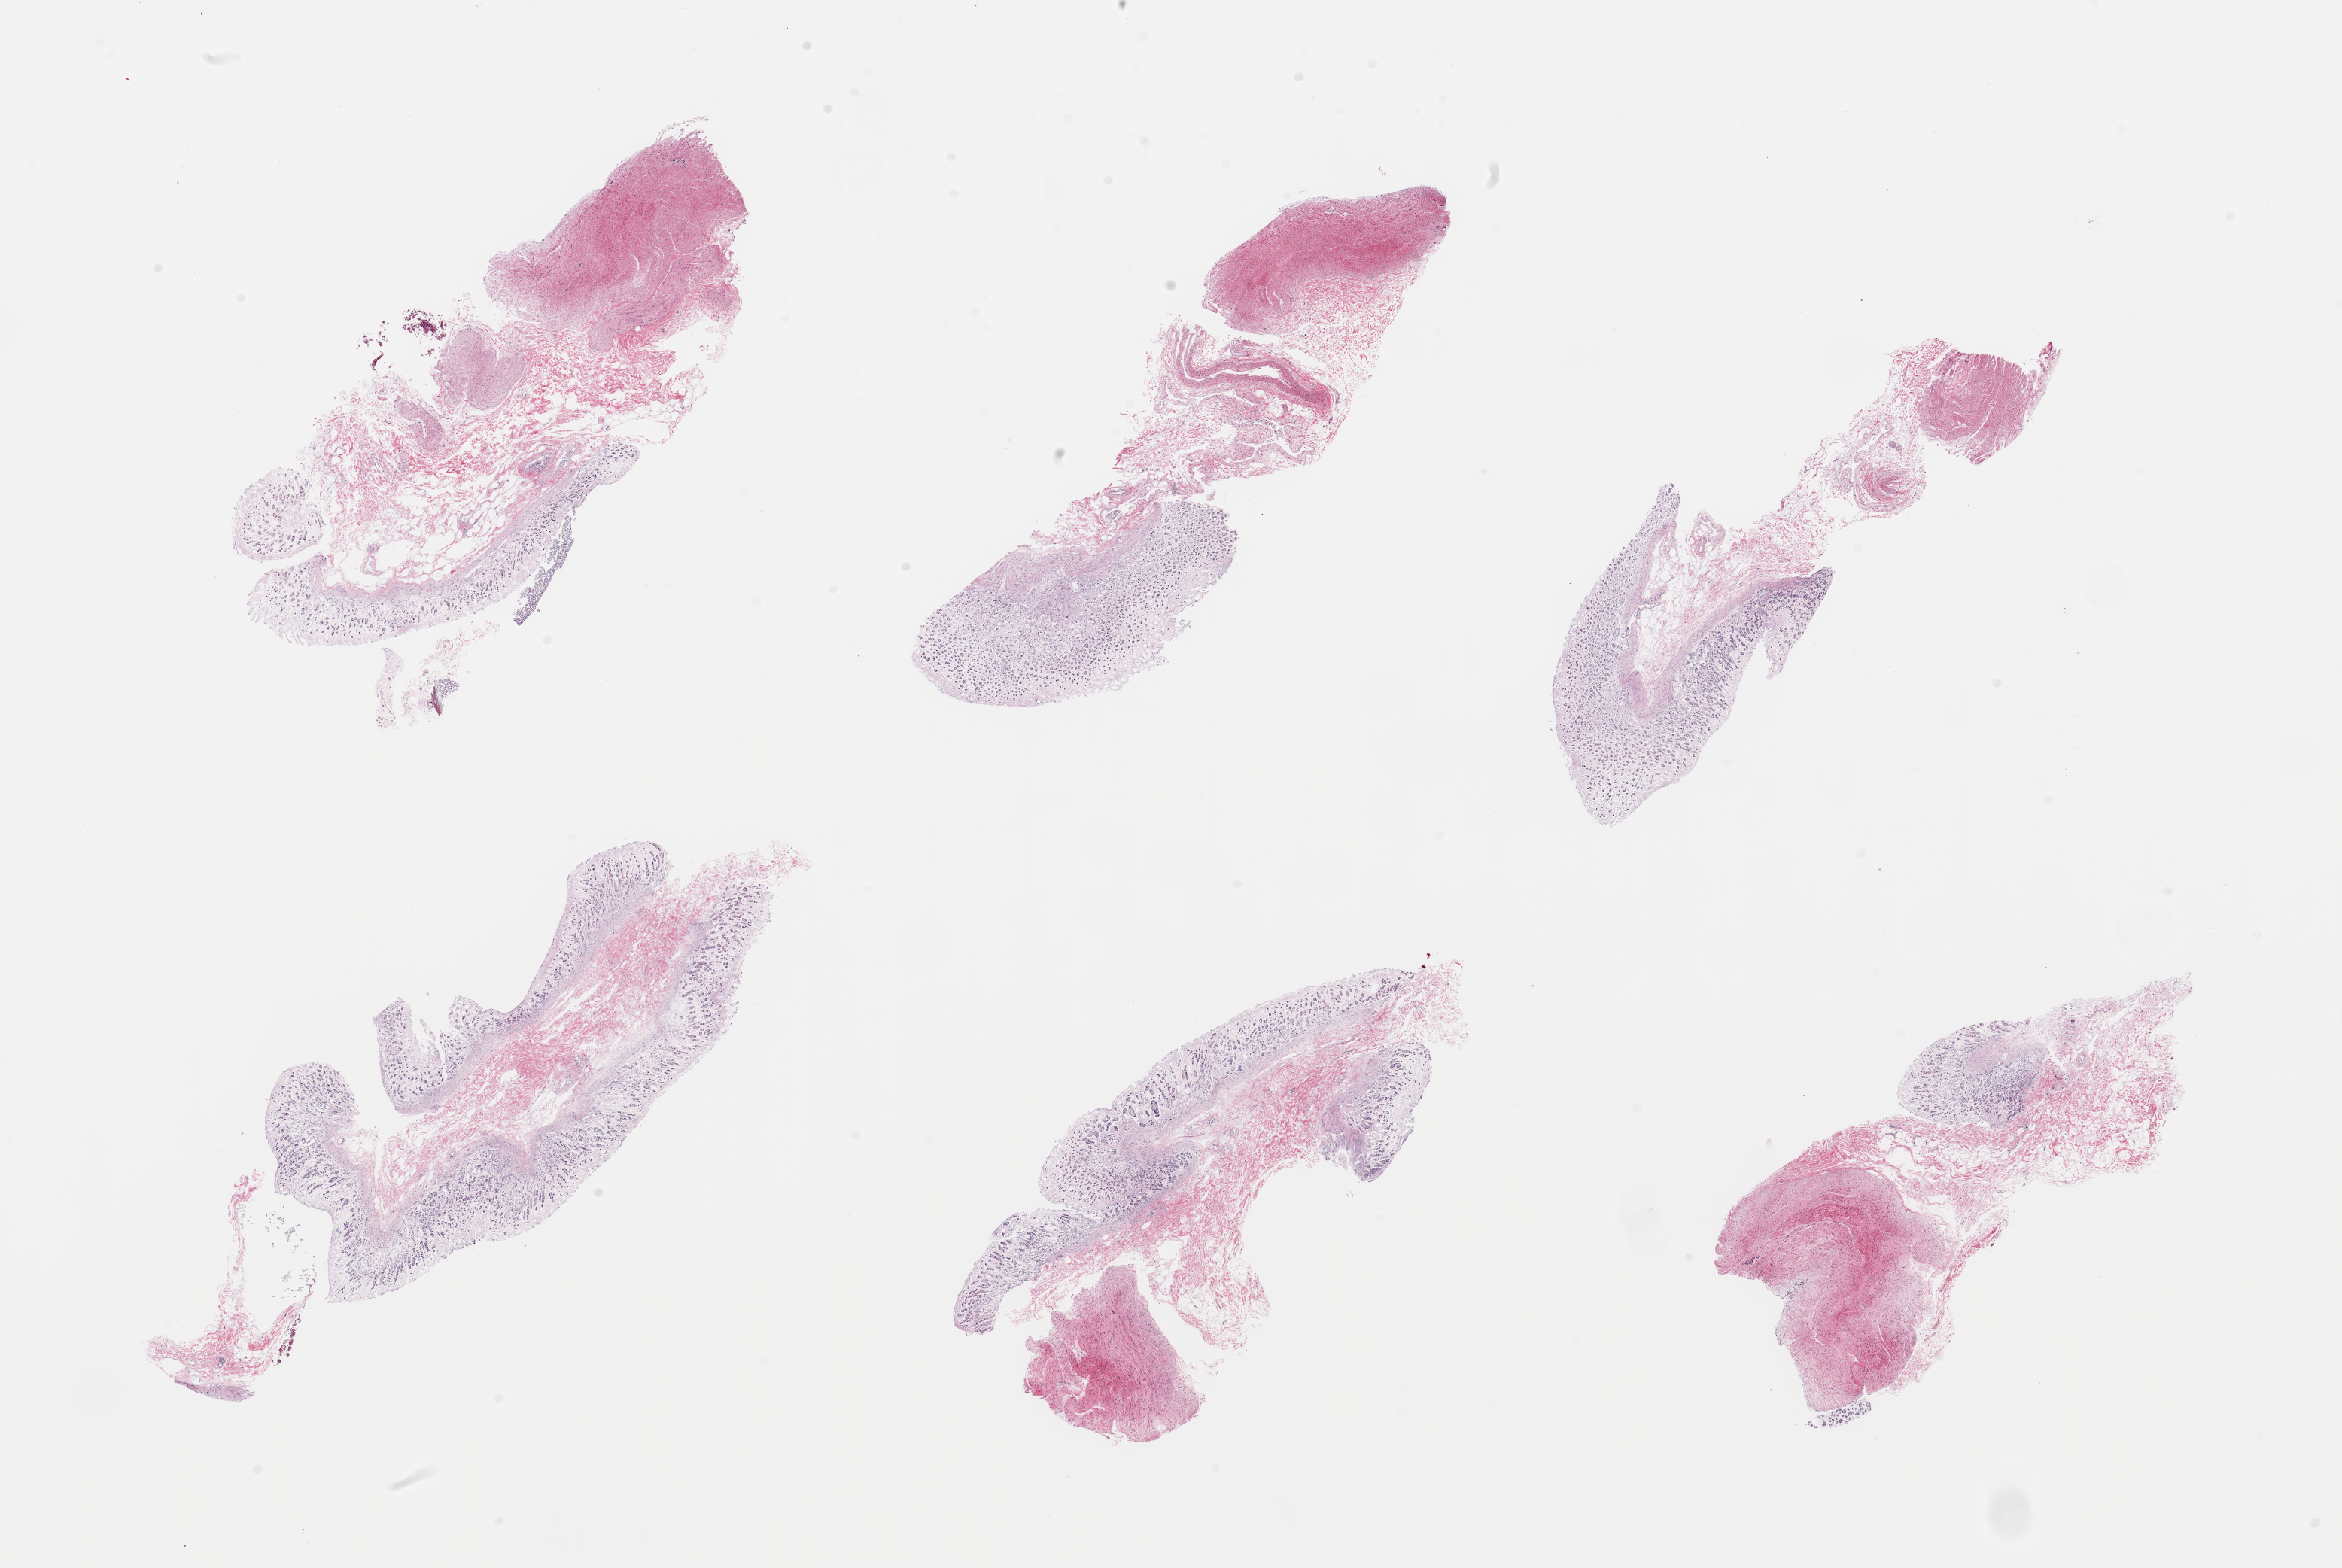
Whole-slide image, haematoxylin and eosin stain — low-resolution overview of the scanned area, about 24.6 x 16.5 mm (from a 20x scan). PAXgene-fixed paraffin-embedded (PFPE) section. Section of stomach (target tissue). Tissue donor sample. Donor: male.
Pathologist's review note for this sample: 6 pieces; entirely autolyzed mucosa and muscularis.